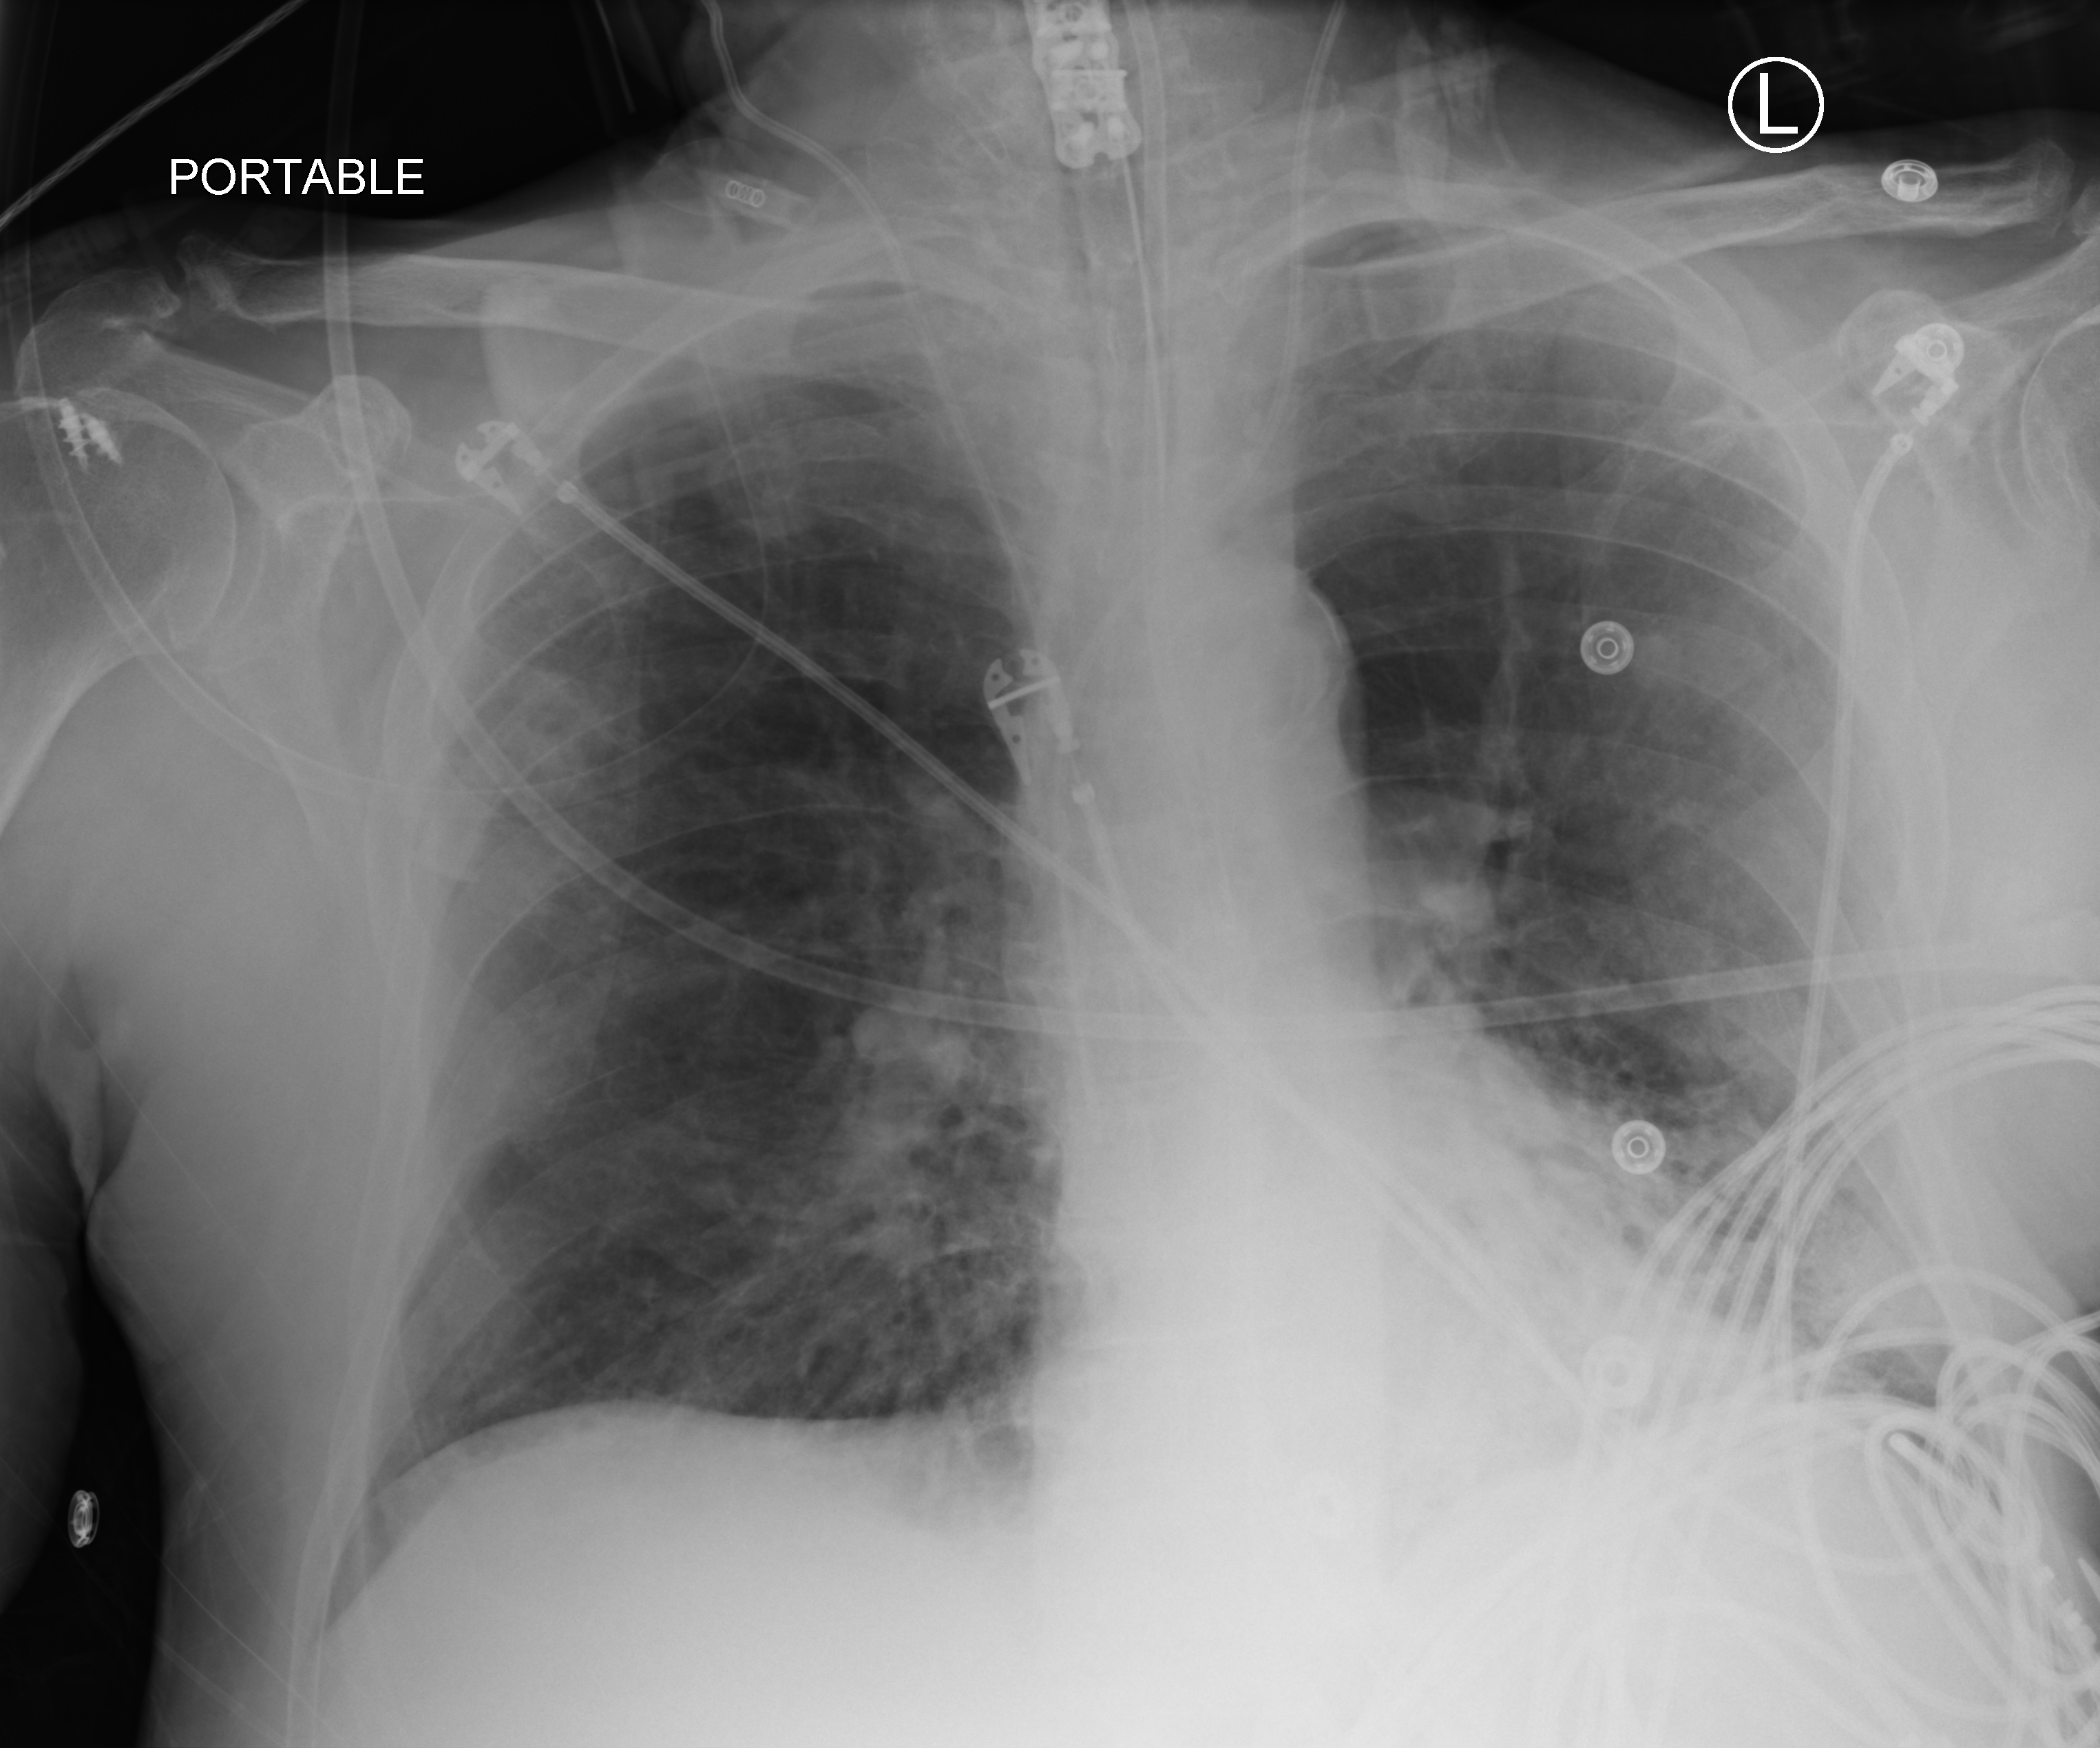
Portable chest radiograph, anteroposterior (AP) projection. Patient hospitalised with COVID-19; male, aged 75–90 years.
Admission-level facts for this patient (not findings on this image; timing relative to this image not recorded):
- COPD (admission record): no
- other chronic lung disease (admission record): no